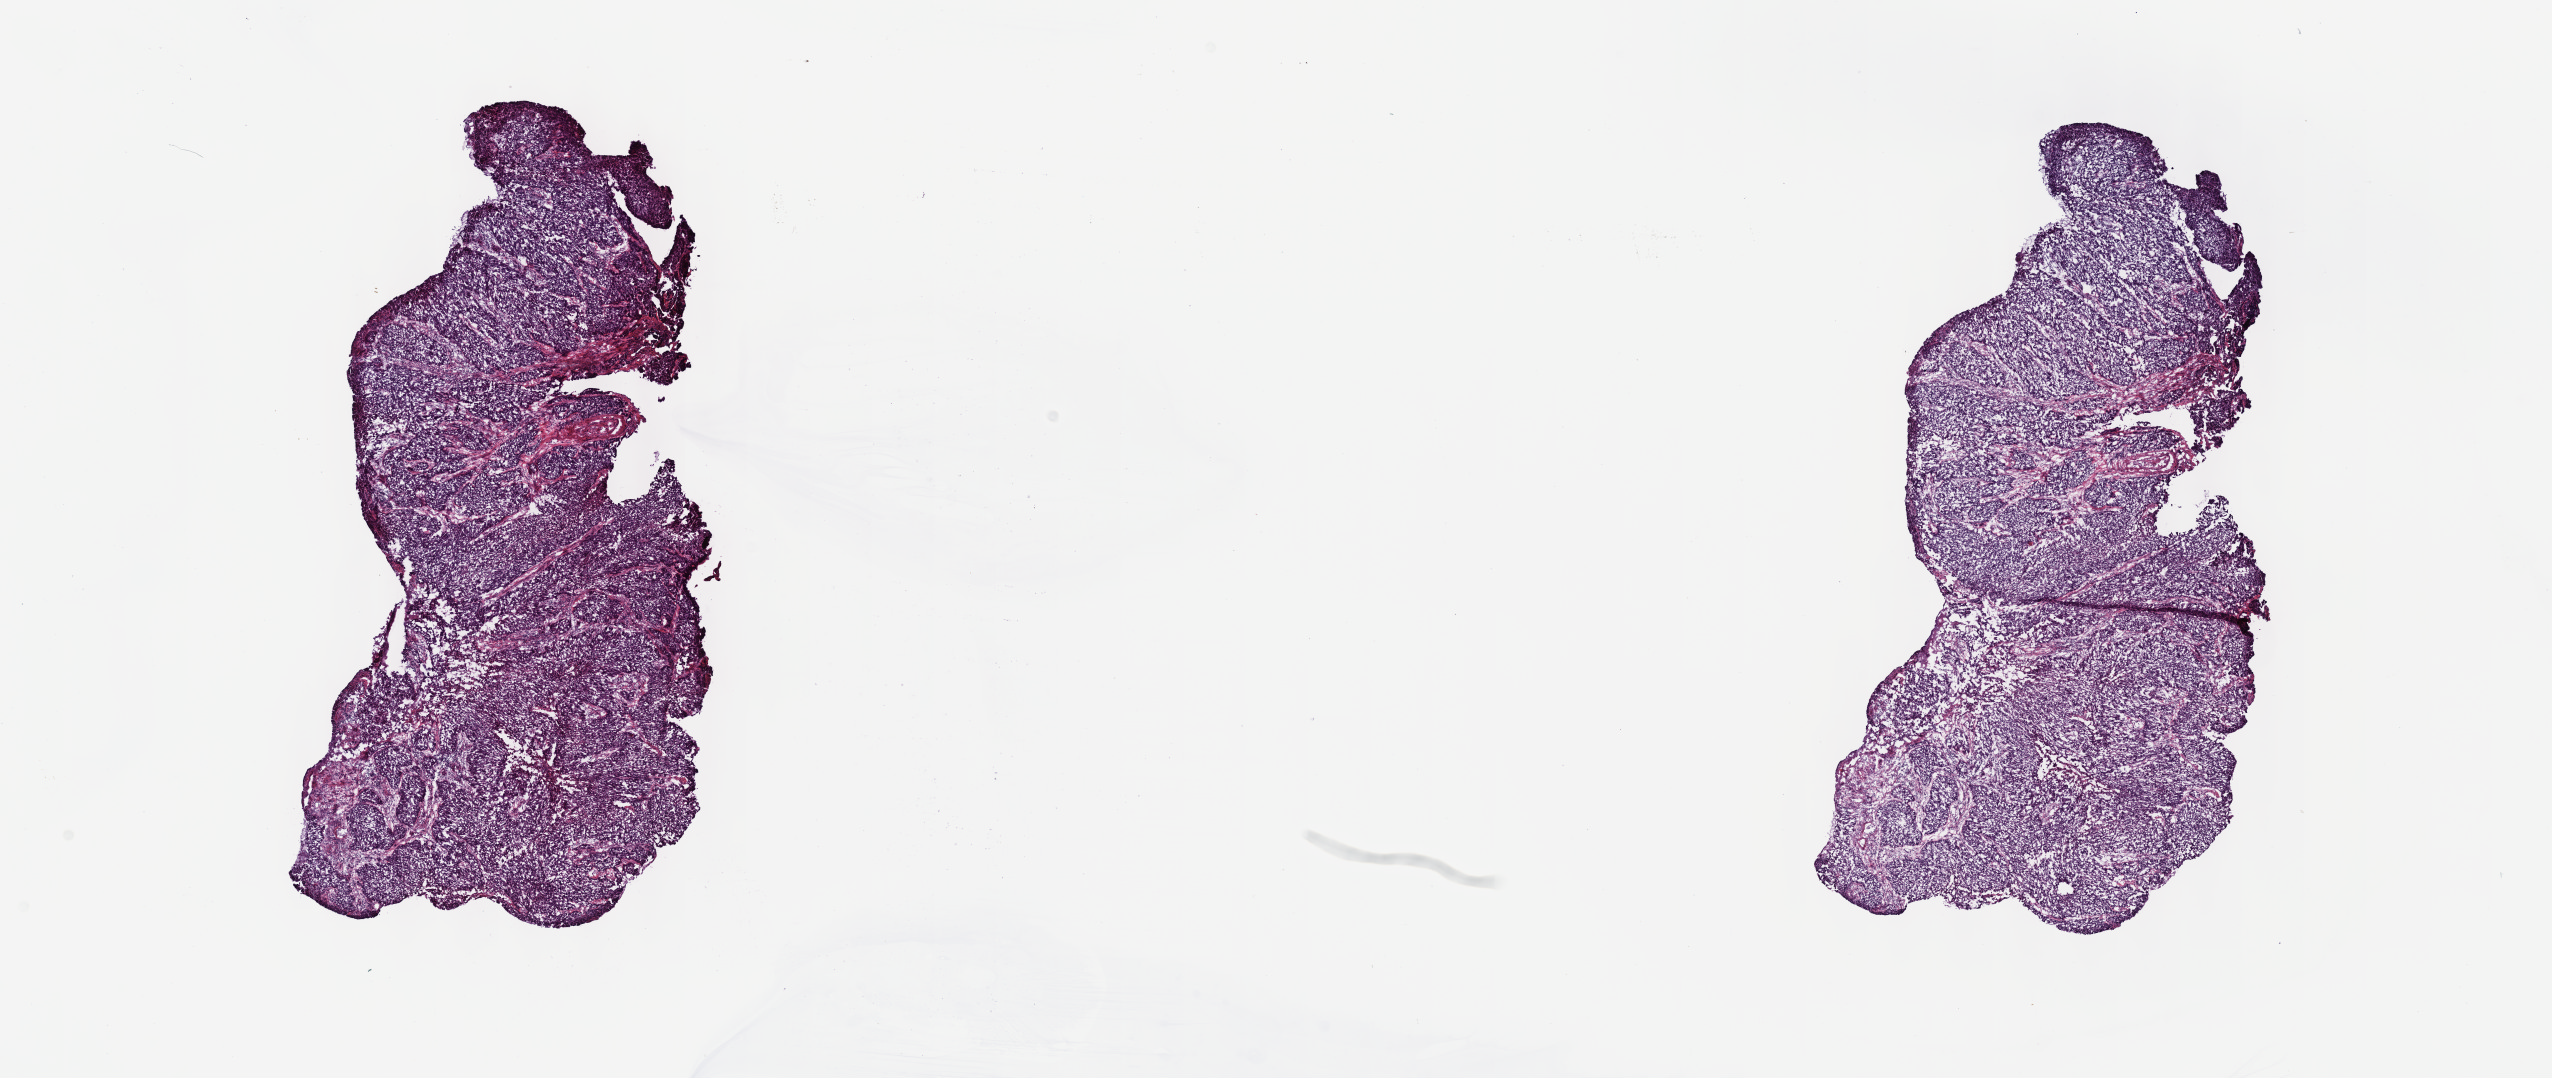
Hematoxylin and eosin (H&E) stained whole-slide image — whole scanned area (about 20.6 x 8.7 mm, from a 40x scan) shown as a low-resolution overview, frozen section from the top of the tissue portion, sample: primary tumour, cervix. Patient: female, age at initial diagnosis 41 years.
Diagnosis: Squamous cell carcinoma, NOS (cervix uteri).